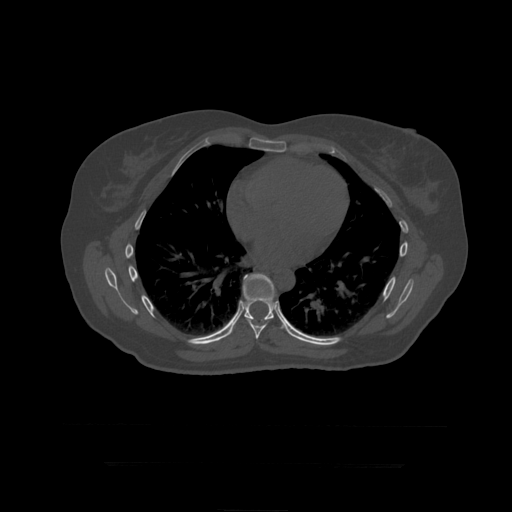
CT including the spine, one axial slice. Position 272 of 399 along the scan axis. 120 kVp. Bone window (W 1800 / L 400 HU). 1.25 mm slice thickness. 512 × 512 image matrix, field of view 450 × 450 mm. Patient age 41 years. From the clinical record (not read from this slice): primary cancer: breast.
Structures marked on this image (semi-automatically segmented with operator editing):
- T8 vertebra: bounding box <244,316,271,340> (left, top, right, bottom; pixels)
- T9 vertebra: <228,274,293,337>